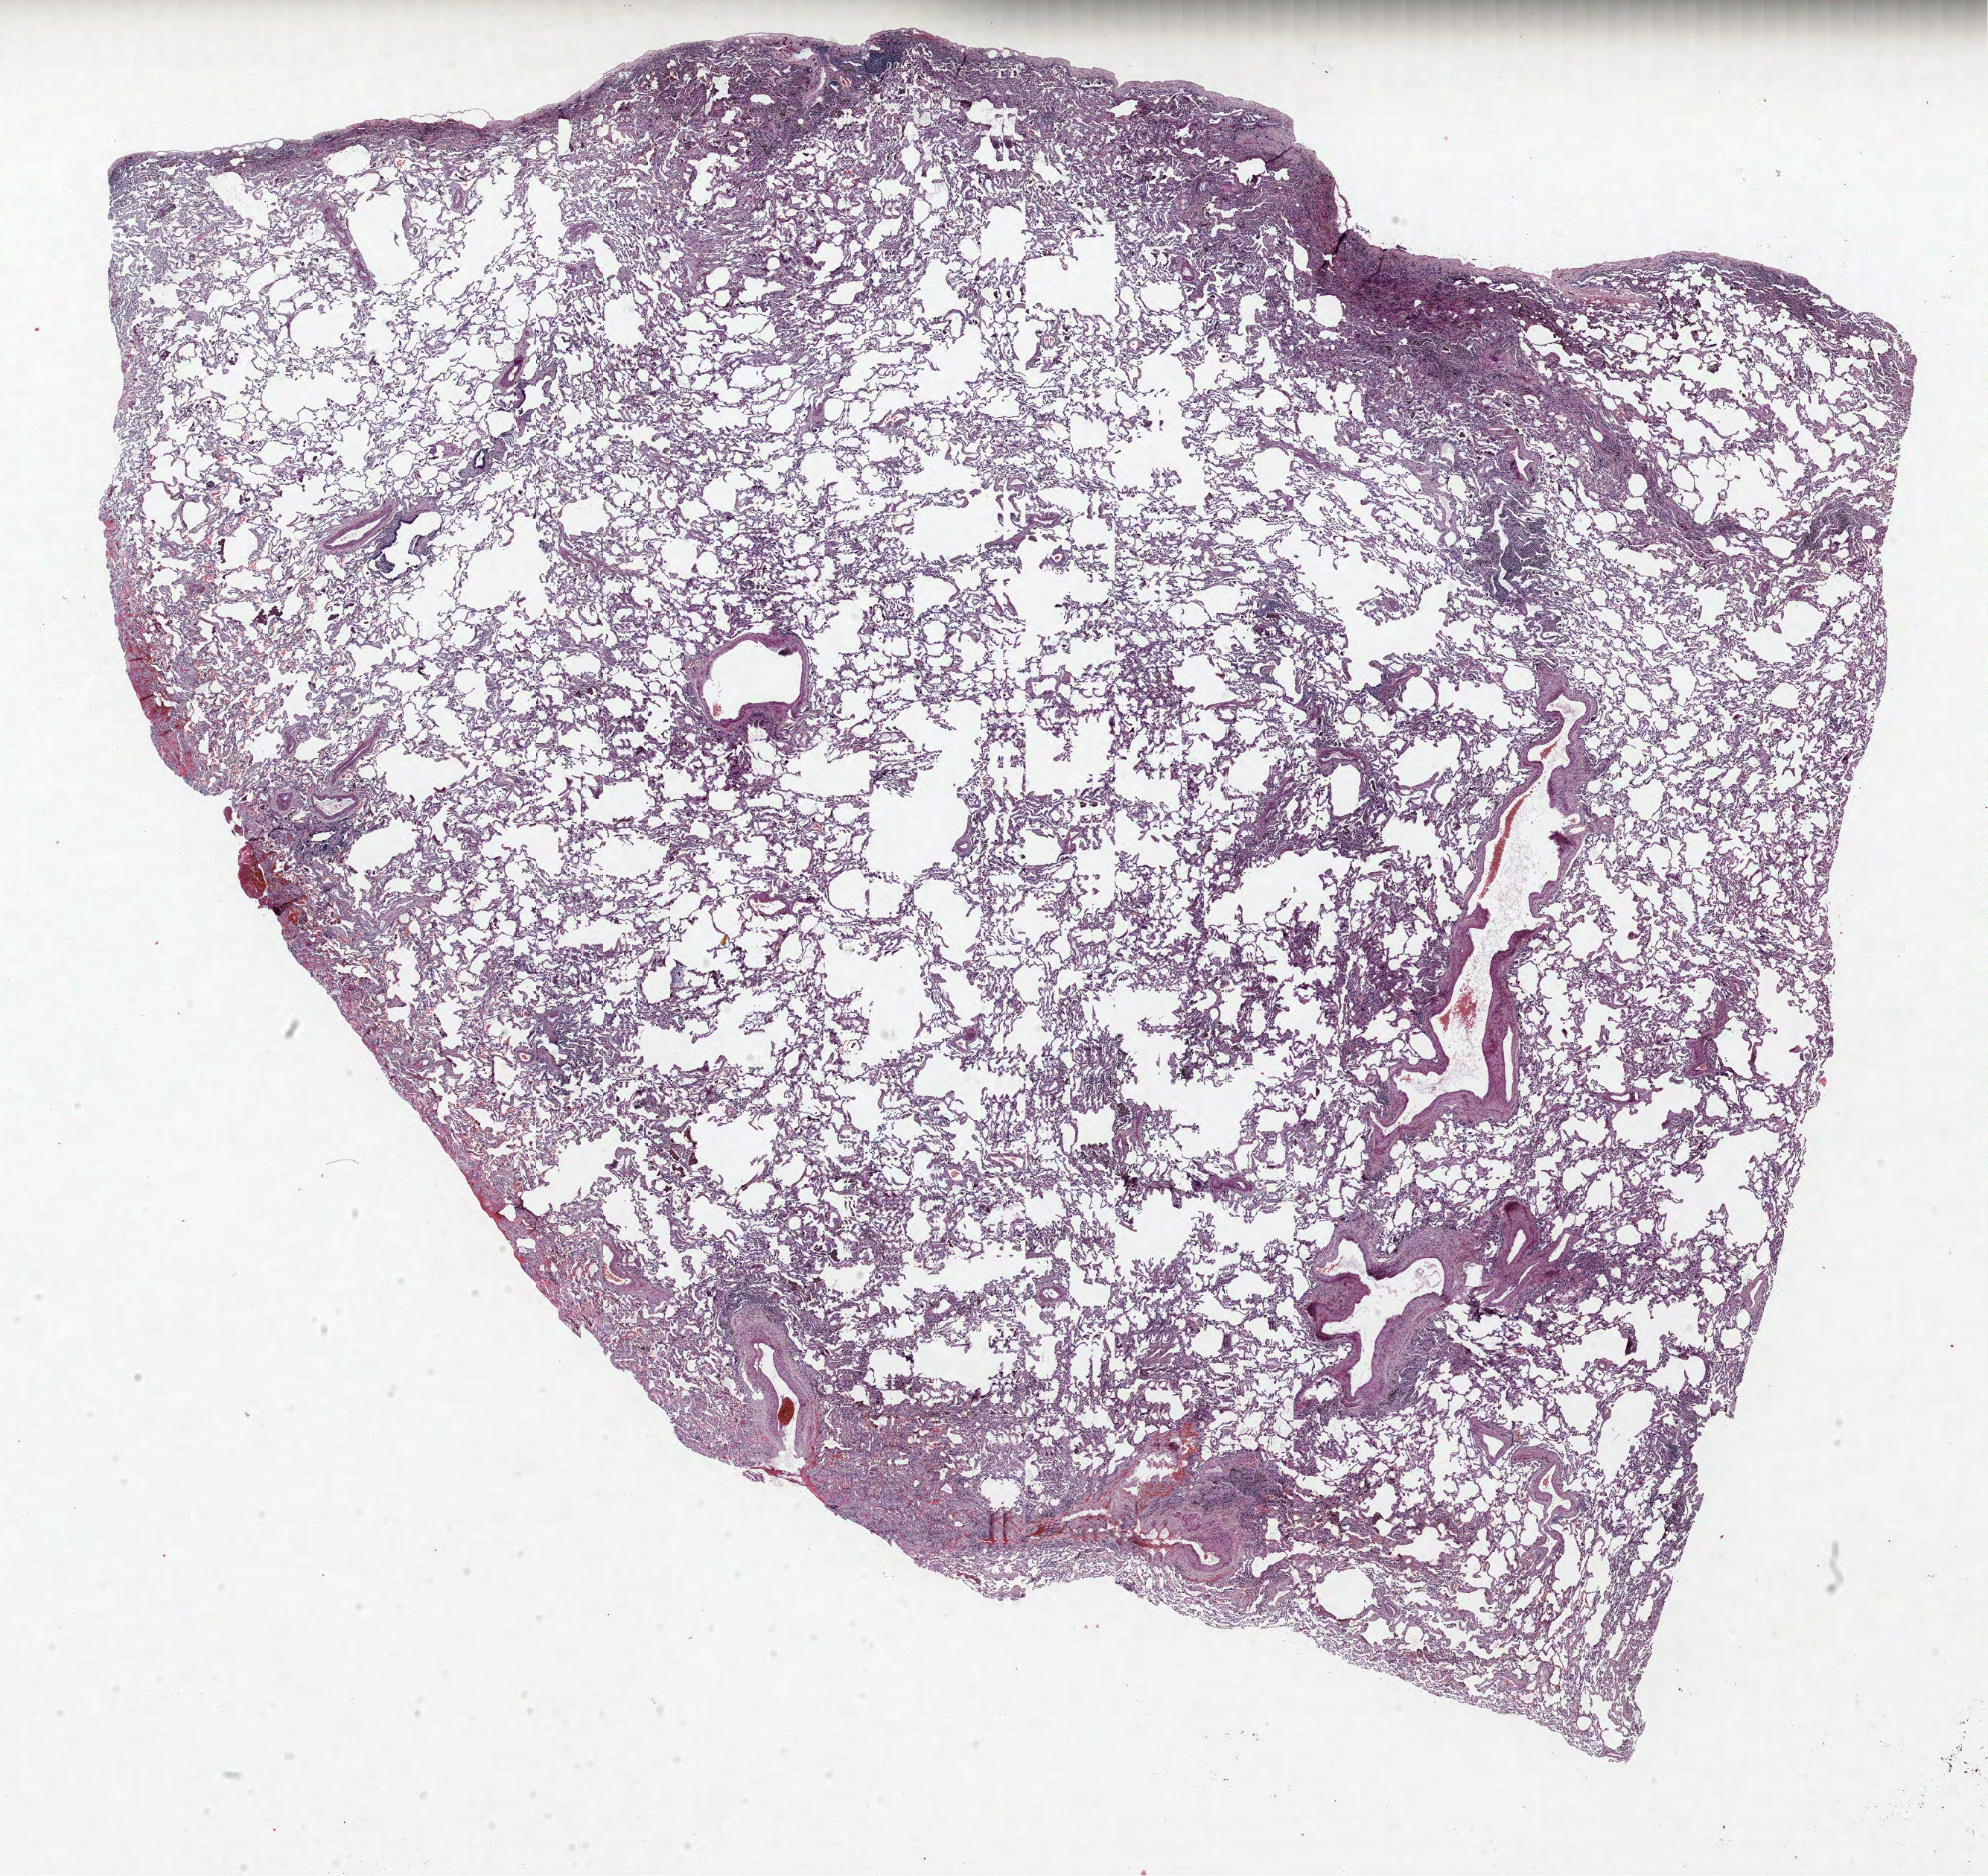
H&E whole-slide image, whole scanned area (about 21.4 x 20.2 mm) shown as a low-resolution overview. FFPE section. Lung tissue. Female patient, aged 55 at enrolment. Grade: poorly differentiated (G3).
Stage (AJCC 6th edition): IA. Tumour size (pathology): 8 mm. Participant's lung-cancer diagnosis: Squamous cell carcinoma, NOS. ICD-O-3 topography: upper lobe of lung (C34.1). Primary tumour location (clinical record): right upper lobe.